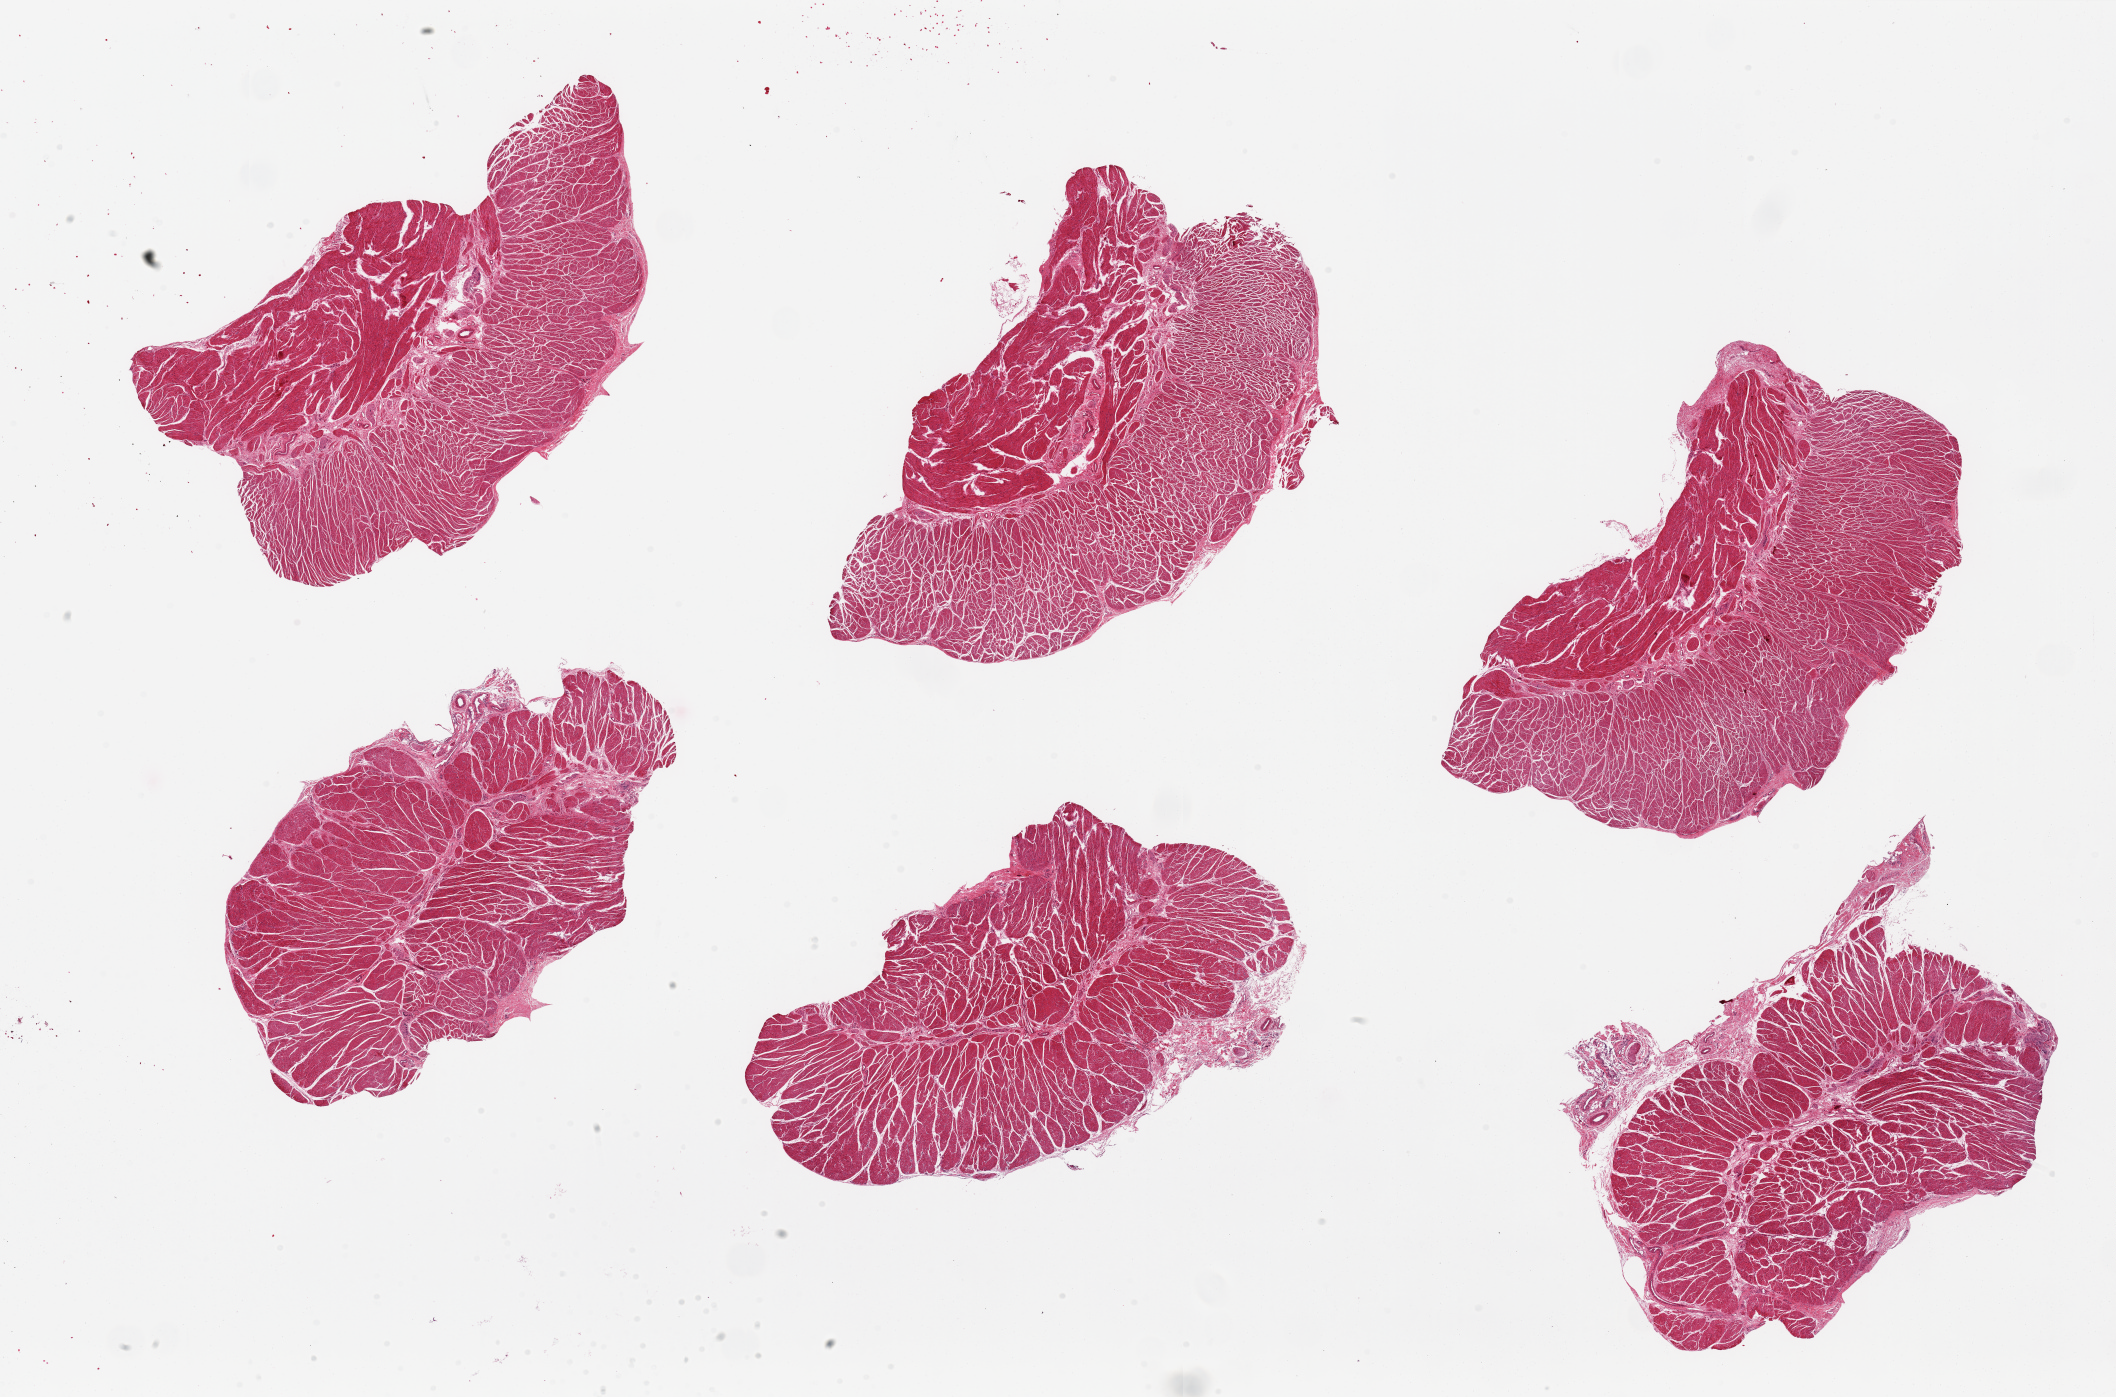
Whole-slide image, H&E stain — whole scanned area (about 33.5 x 22.1 mm) shown as a low-resolution overview, PAXgene-fixed paraffin-embedded (PFPE) section, sampled site (target tissue): gastroesophageal junction, tissue donor sample. Female donor.
- reviewer comment on this tissue sample: 6 pieces. up to 9x7mm; Well trimmed muscularis